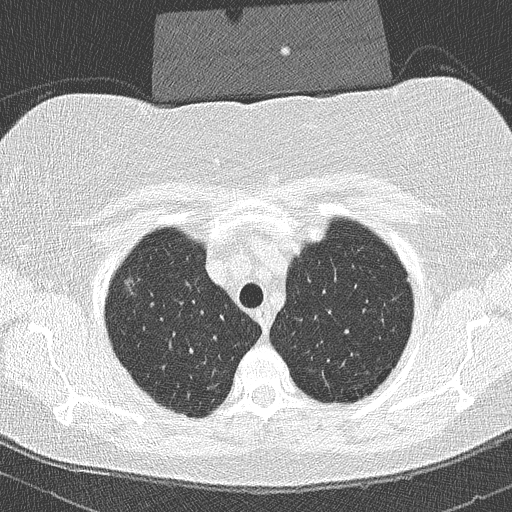
Chest CT (low-dose screening protocol), one axial image, second screening round (one year after baseline), lung window (W 1500 / L -600 HU), lung (sharp) reconstruction kernel (B50f), 120 kVp, slice 39 of 293 in the series, 512 × 512 image matrix. Female, age 58 years at enrolment. Former smoker at enrolment.
Lesion marked by an expert reader, bounding box [x1, y1, x2, y2] px = [110, 270, 151, 303]. The screening reader recorded 2 non-calcified nodules or masses ≥4 mm on this exam (right upper lobe, right upper lobe); which of them this box marks is not recorded. Later outcome: lung cancer diagnosed 447 days after this screen (after the third annual screen) — bronchiolo-alveolar adenocarcinoma, NOS, right upper lobe, well differentiated (G1), stage IA (AJCC 6th edition), 9 mm at pathology.